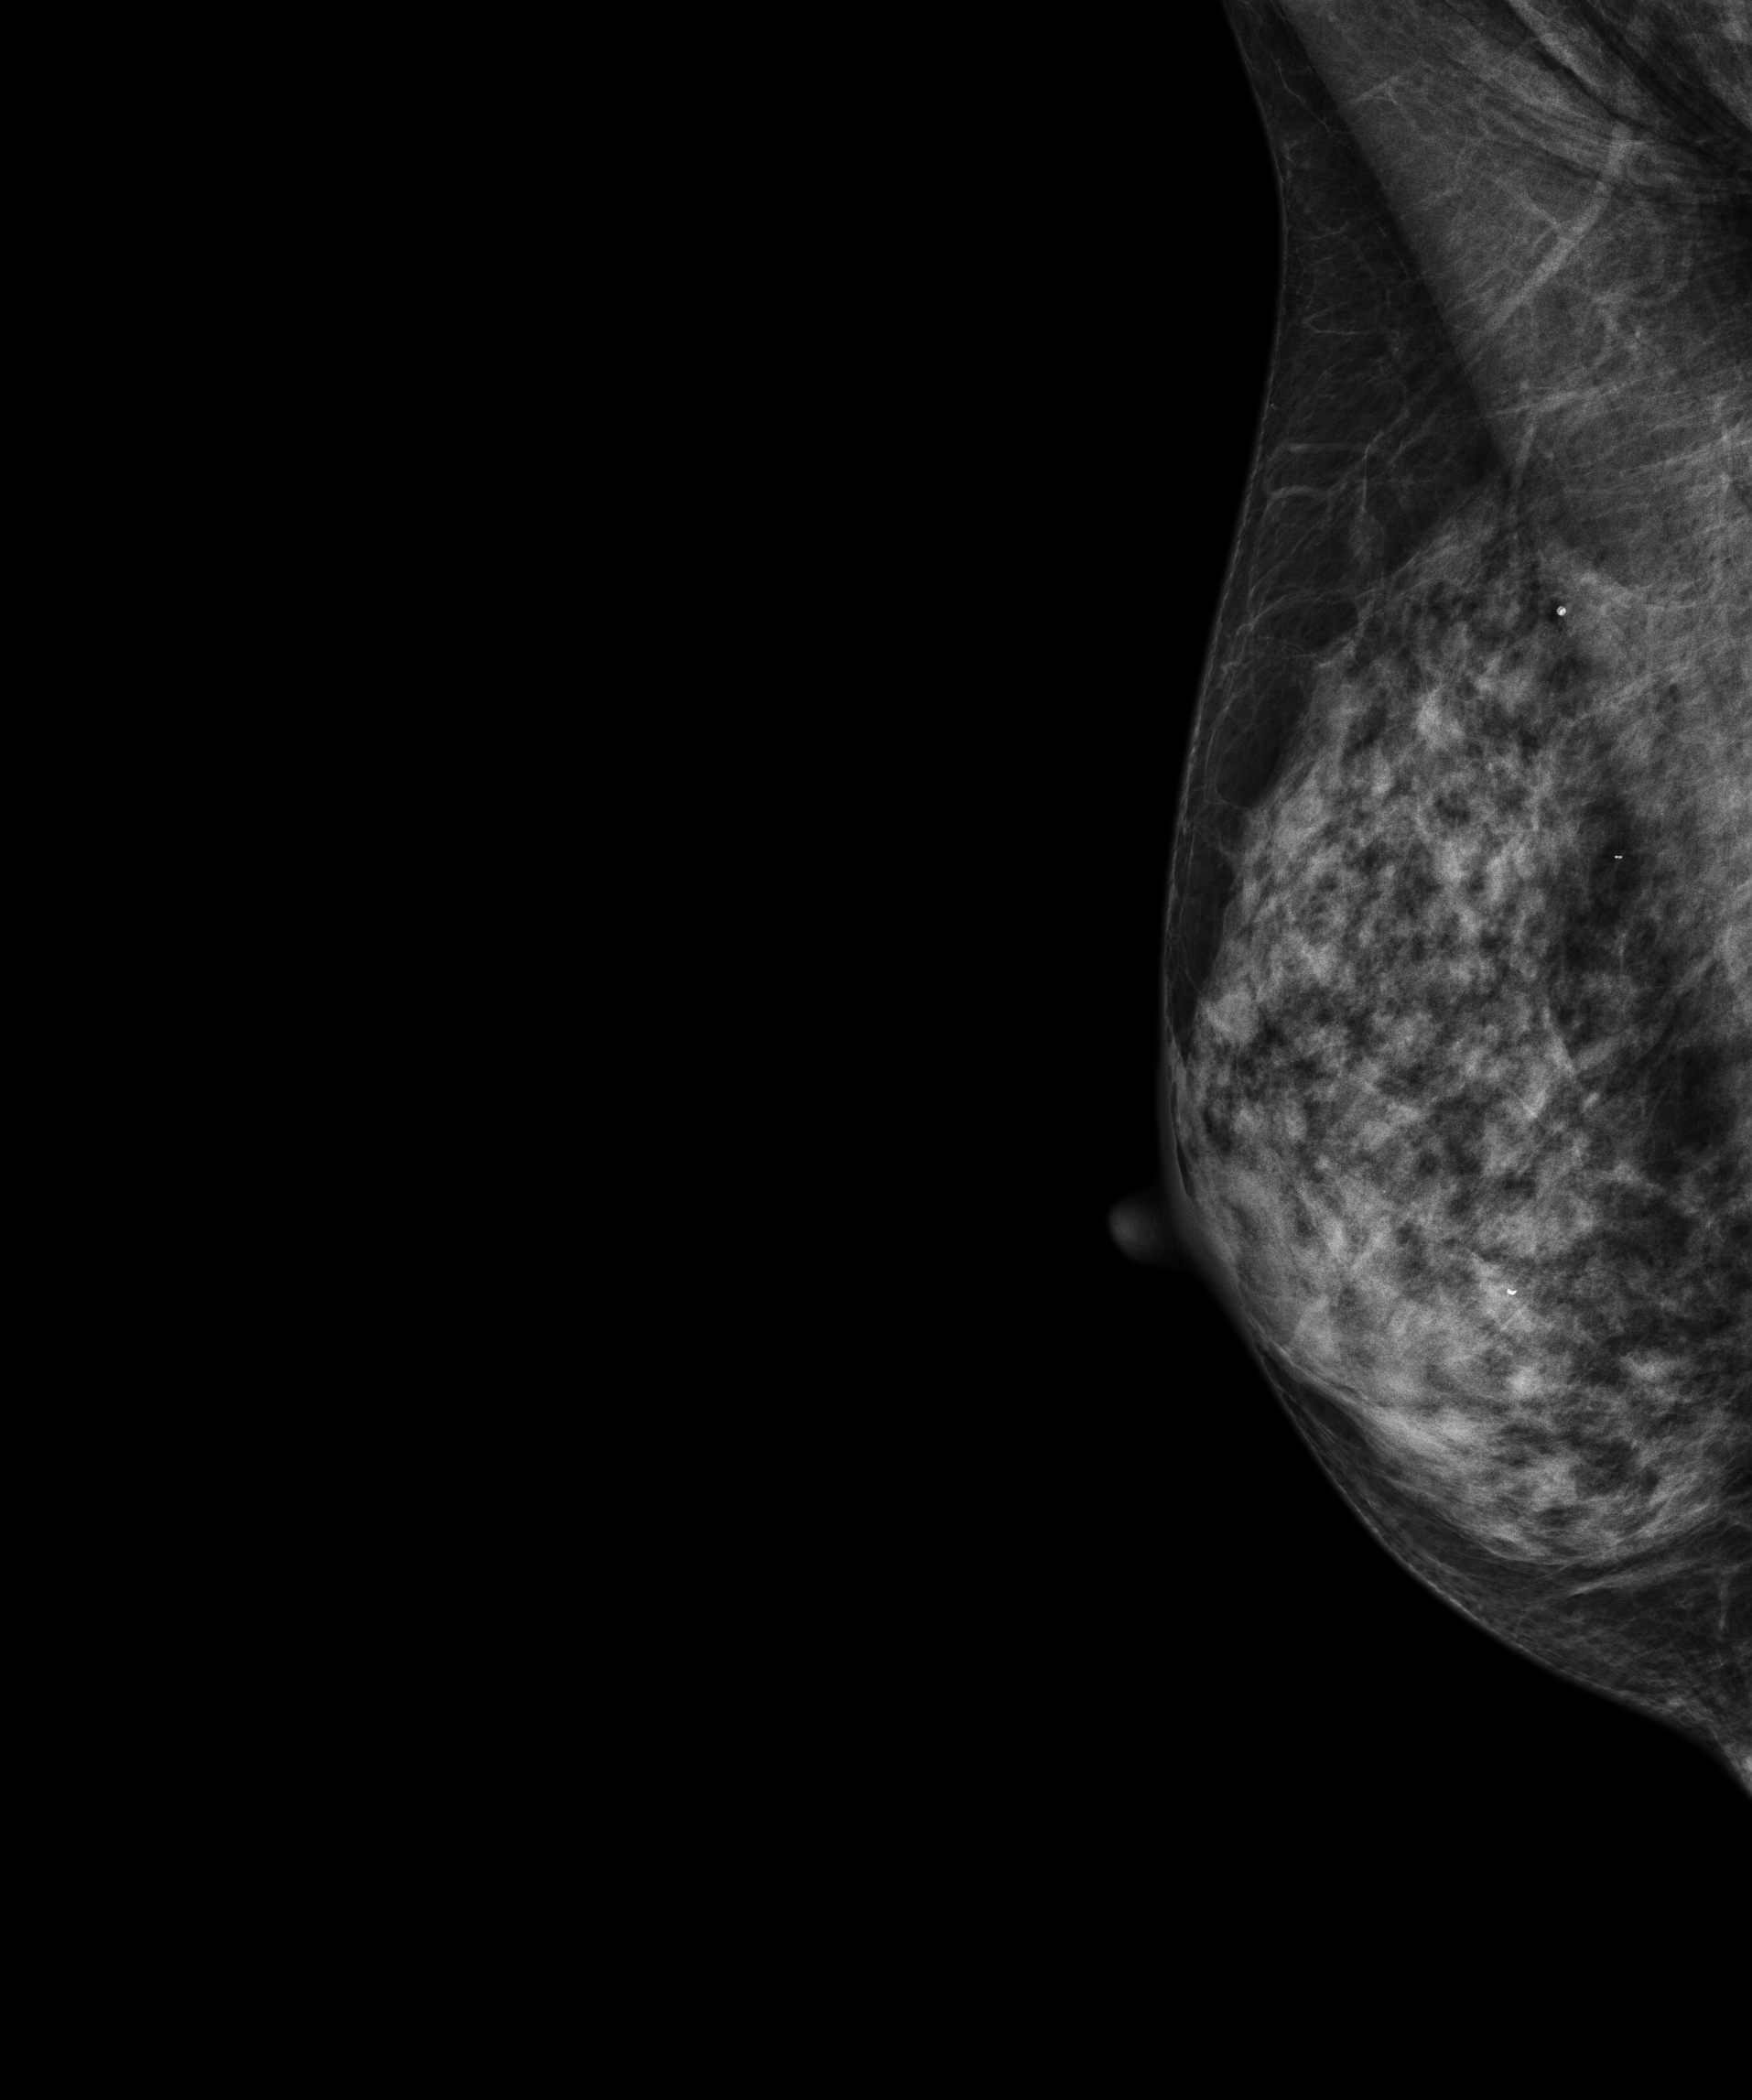
Full-field digital mammogram (FFDM); right breast; MLO view; screening examination; compressed breast thickness 40 mm; system: Senographe Essential ADS_56.21.3. Patient aged 67 years (female).
- BI-RADS breast density category at the screening exam (both breasts, scale 1–4): 3
- final BI-RADS category for the screening round (tomosynthesis exam, both breasts): category 1
- recall: no recall after this screen